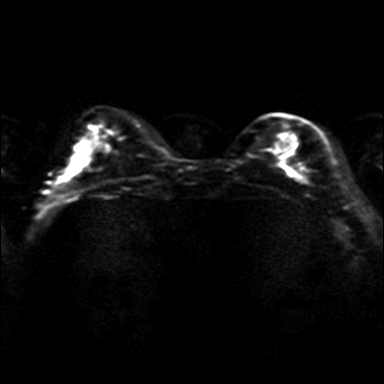
Breast MRI, one axial slice. Position 10 of 36 along the scan axis. Diffusion-weighted series; image 2 of 4 stored at this slice position (different b-values; order by instance number). 3 T. 4 mm slice thickness. 384 × 384 image matrix, field of view 320 × 320 mm. Female patient.
Outlined on this slice (outlined manually by an expert reader):
- tumour on diffusion-weighted imaging: bounding box <295,172,304,180> (left, top, right, bottom; pixels)